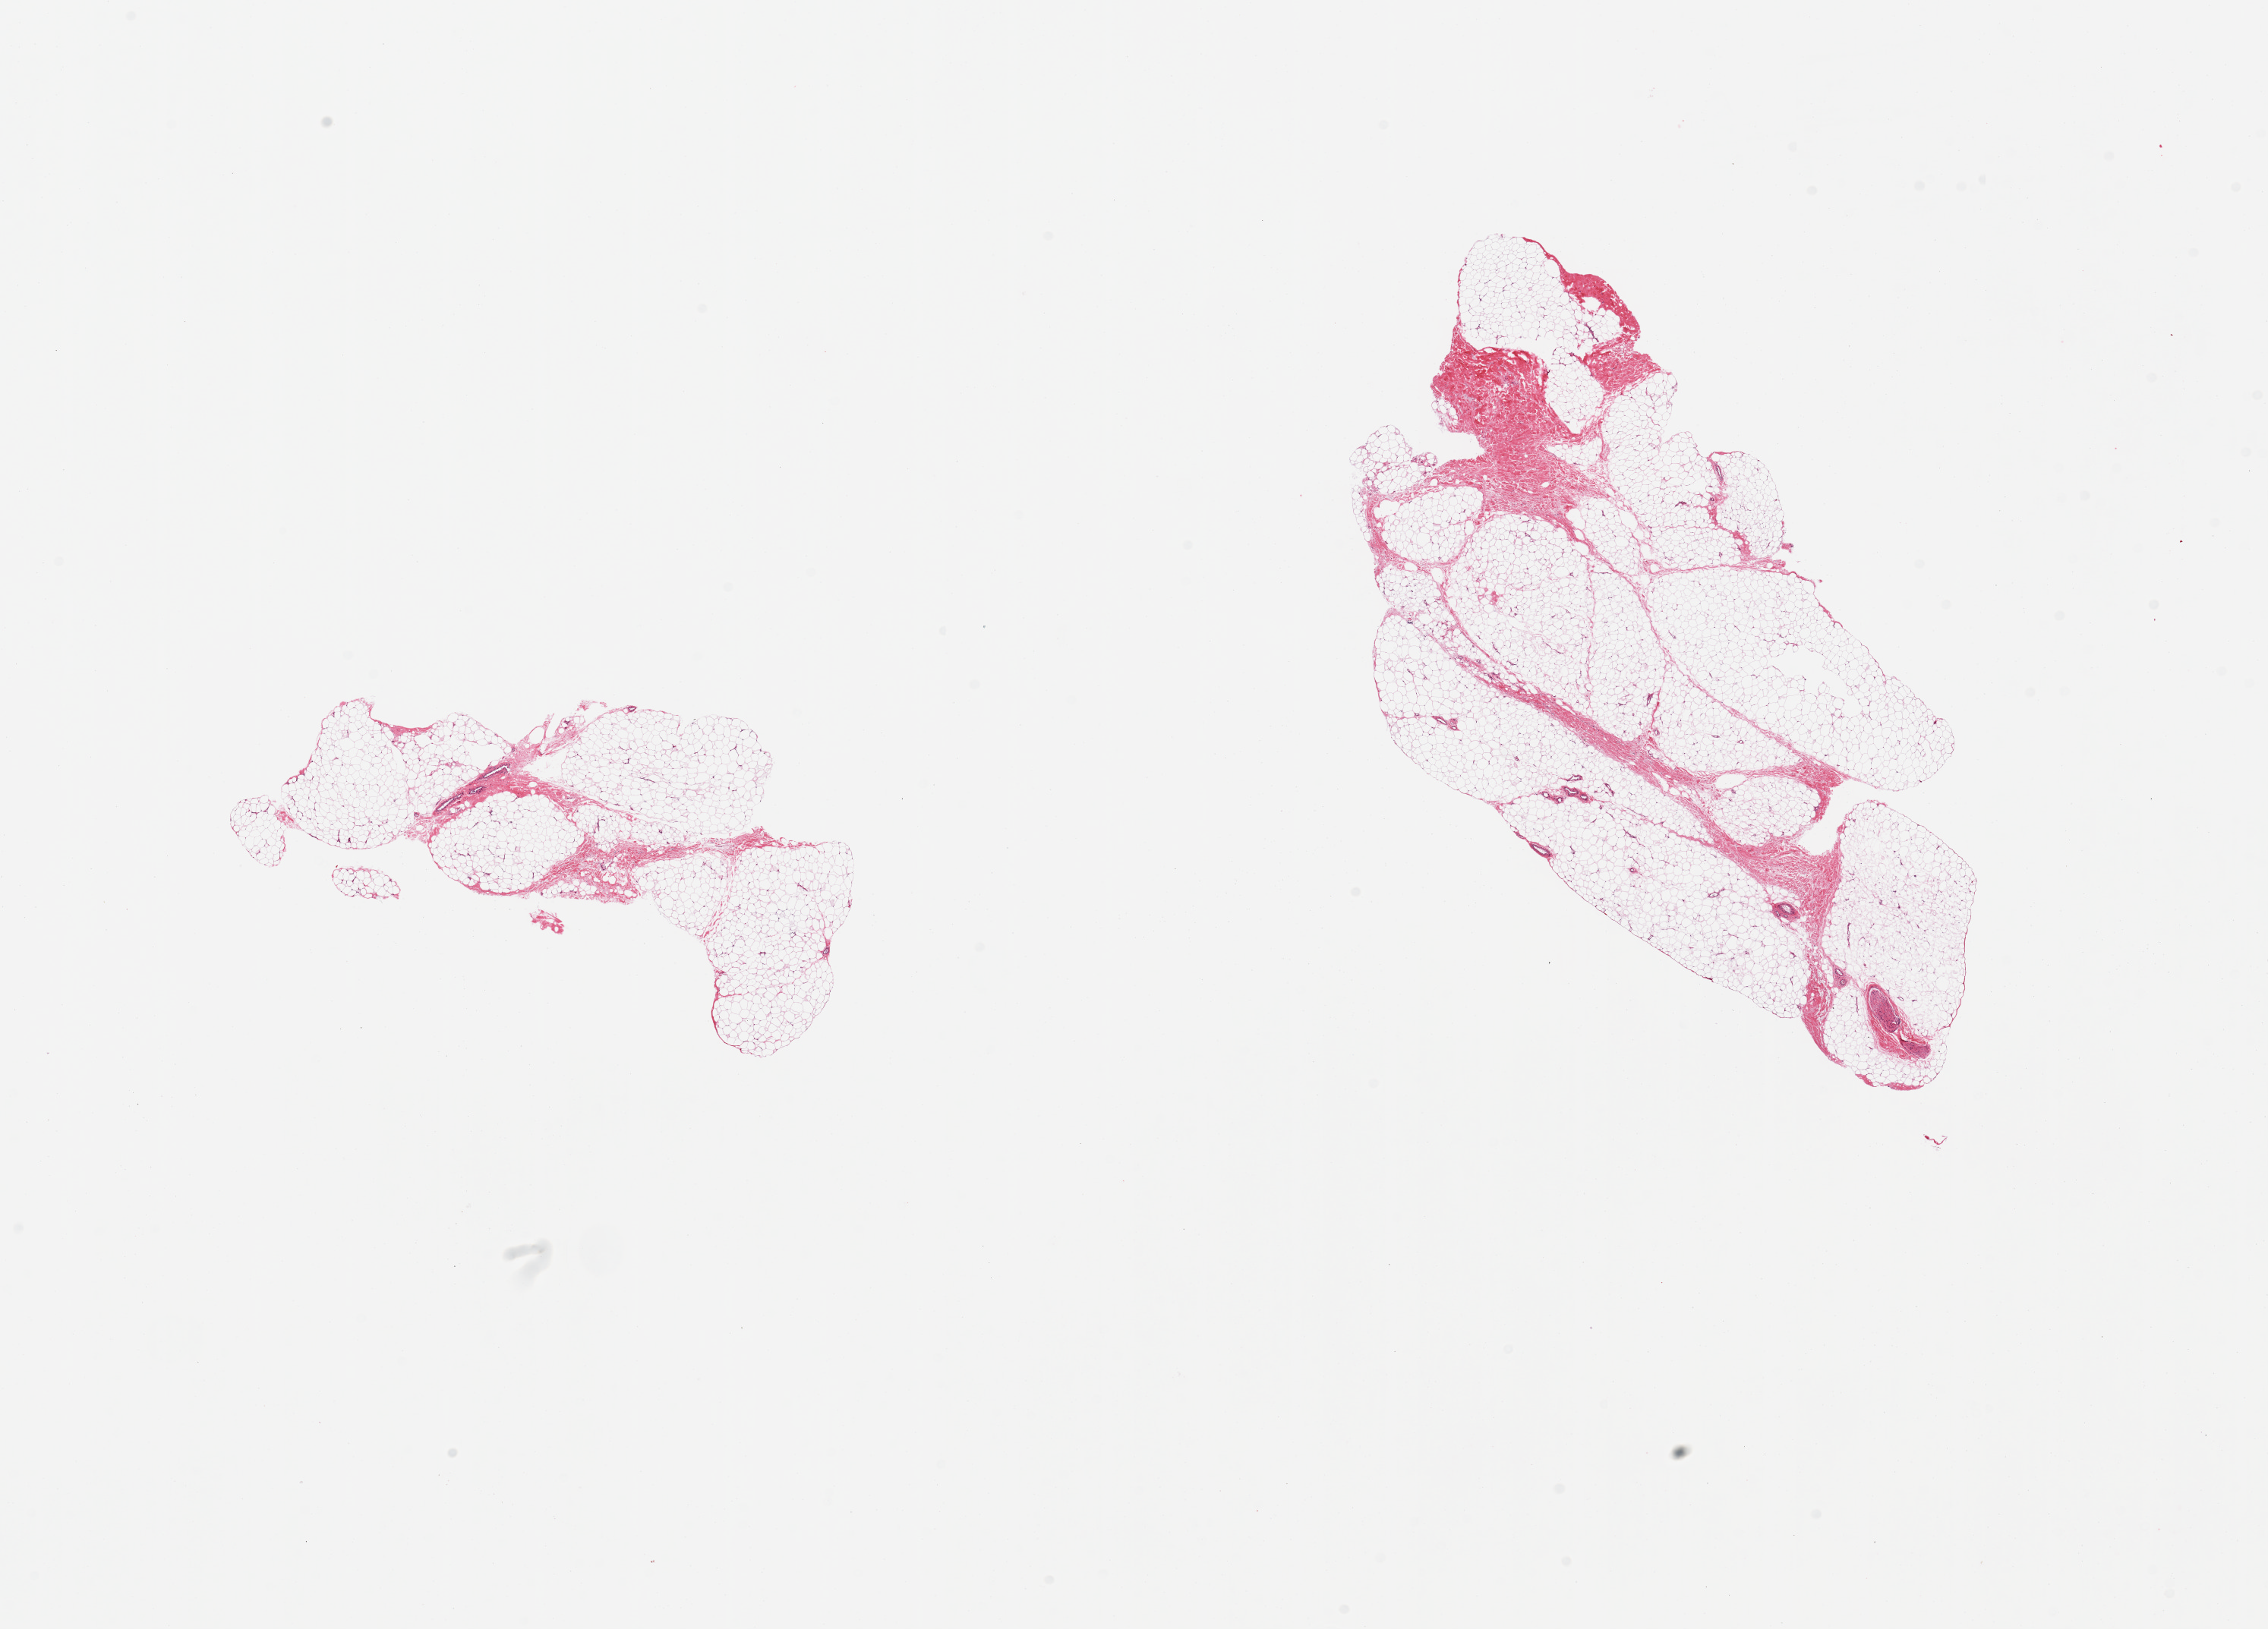
Digitized hematoxylin and eosin (H&E)-stained section — a low-resolution overview of the entire scanned area, about 23.6 x 17.0 mm, PAXgene-fixed paraffin-embedded (PFPE) section, section of adipose tissue (target tissue), tissue donor sample. Donor sex: male.
Pathologist's review note for this sample: 2 pieces, no abnormalities, ~15% fascia/fibrous tissue.